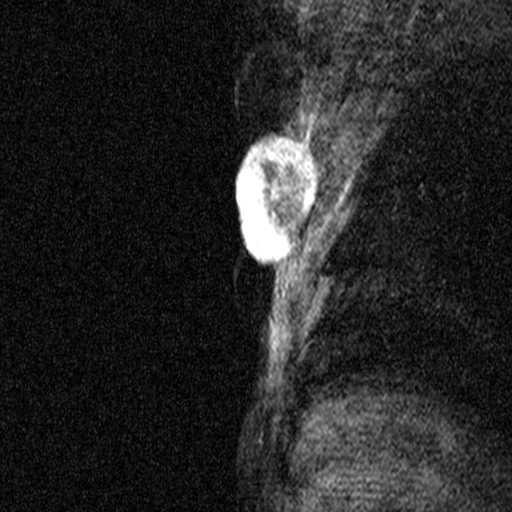
Breast MRI (dynamic contrast-enhanced), one sagittal slice. Dynamic contrast-enhanced study with each time point stored as its own series, time point 2 of 3 at this slice position (early post-contrast, ordered by acquisition time). 1.5 T. TE 4.5 ms, TR 11 ms. 3 mm slice thickness. 512 × 512 image matrix, field of view 200 × 200 mm. Patient: female, 44 years. From the clinical record (not read from this slice): setting: breast cancer imaged before/during neoadjuvant chemotherapy; receptor status: HR-positive, HER2-negative.
Outlined on this slice (semi-automatic segmentation, software-assisted and operator-edited):
- analysis volume of interest (the breast-tissue region the enhancement analysis was run in; not a lesion): bounding box <218,118,321,291> (left, top, right, bottom; pixels)
- tumour enhancement mask (voxels above the 90 % enhancement threshold inside the analysis volume of interest): <235,135,321,260>